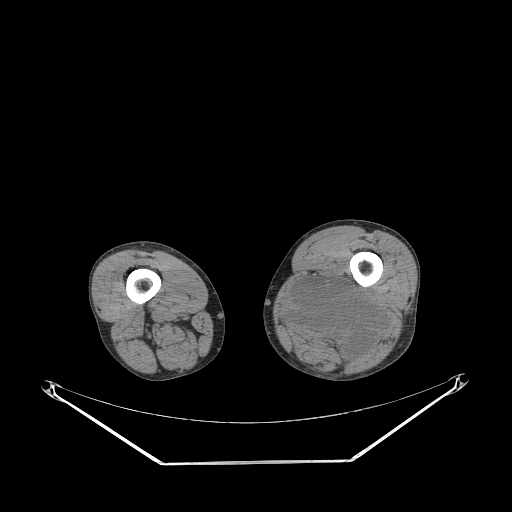
CT of an extremity soft-tissue mass (from a PET/CT study), one axial slice. Position 216 of 267 along the scan axis. 140 kVp. Soft-tissue window (W 400 / L 40 HU). 3.75 mm slice thickness. 512 × 512 image matrix, field of view 500 × 500 mm. Male patient. Case-level facts recorded for this patient, not image findings: histological type: undifferentiated pleomorphic liposarcoma; grade: high; site of the primary tumour: left thigh.
Annotated regions visible in this slice (expert contour drawn on MRI and transferred to this co-registered scan by the dataset authors):
- gross tumour volume including surrounding oedema: bounding box <285,272,384,359> (left, top, right, bottom; pixels)
- gross tumour volume (mass): <285,279,384,359>